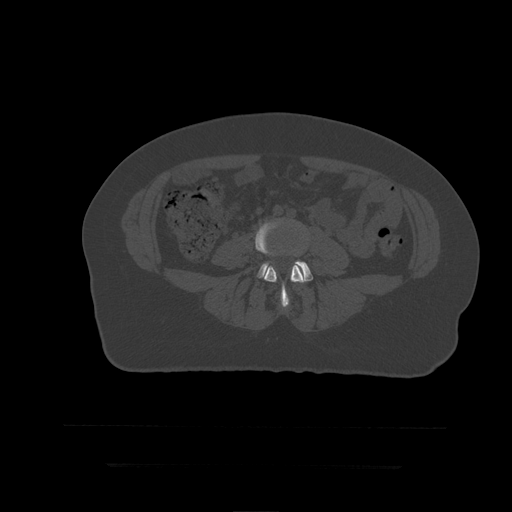
CT including the spine, one axial slice. Slice 87 of 399 in the series (ordered by position). Bone window (W 1800 / L 400 HU). 1.25 mm slice thickness. 512 × 512 image matrix. Patient age 41 years. From the clinical record (not read from this slice): primary cancer: breast.
Annotated regions visible in this slice (semi-automatically segmented with operator editing):
- L4 vertebra: box from (x=256, y=218) to (x=307, y=308) px
- L5 vertebra: (x=257, y=261)–(x=313, y=282)